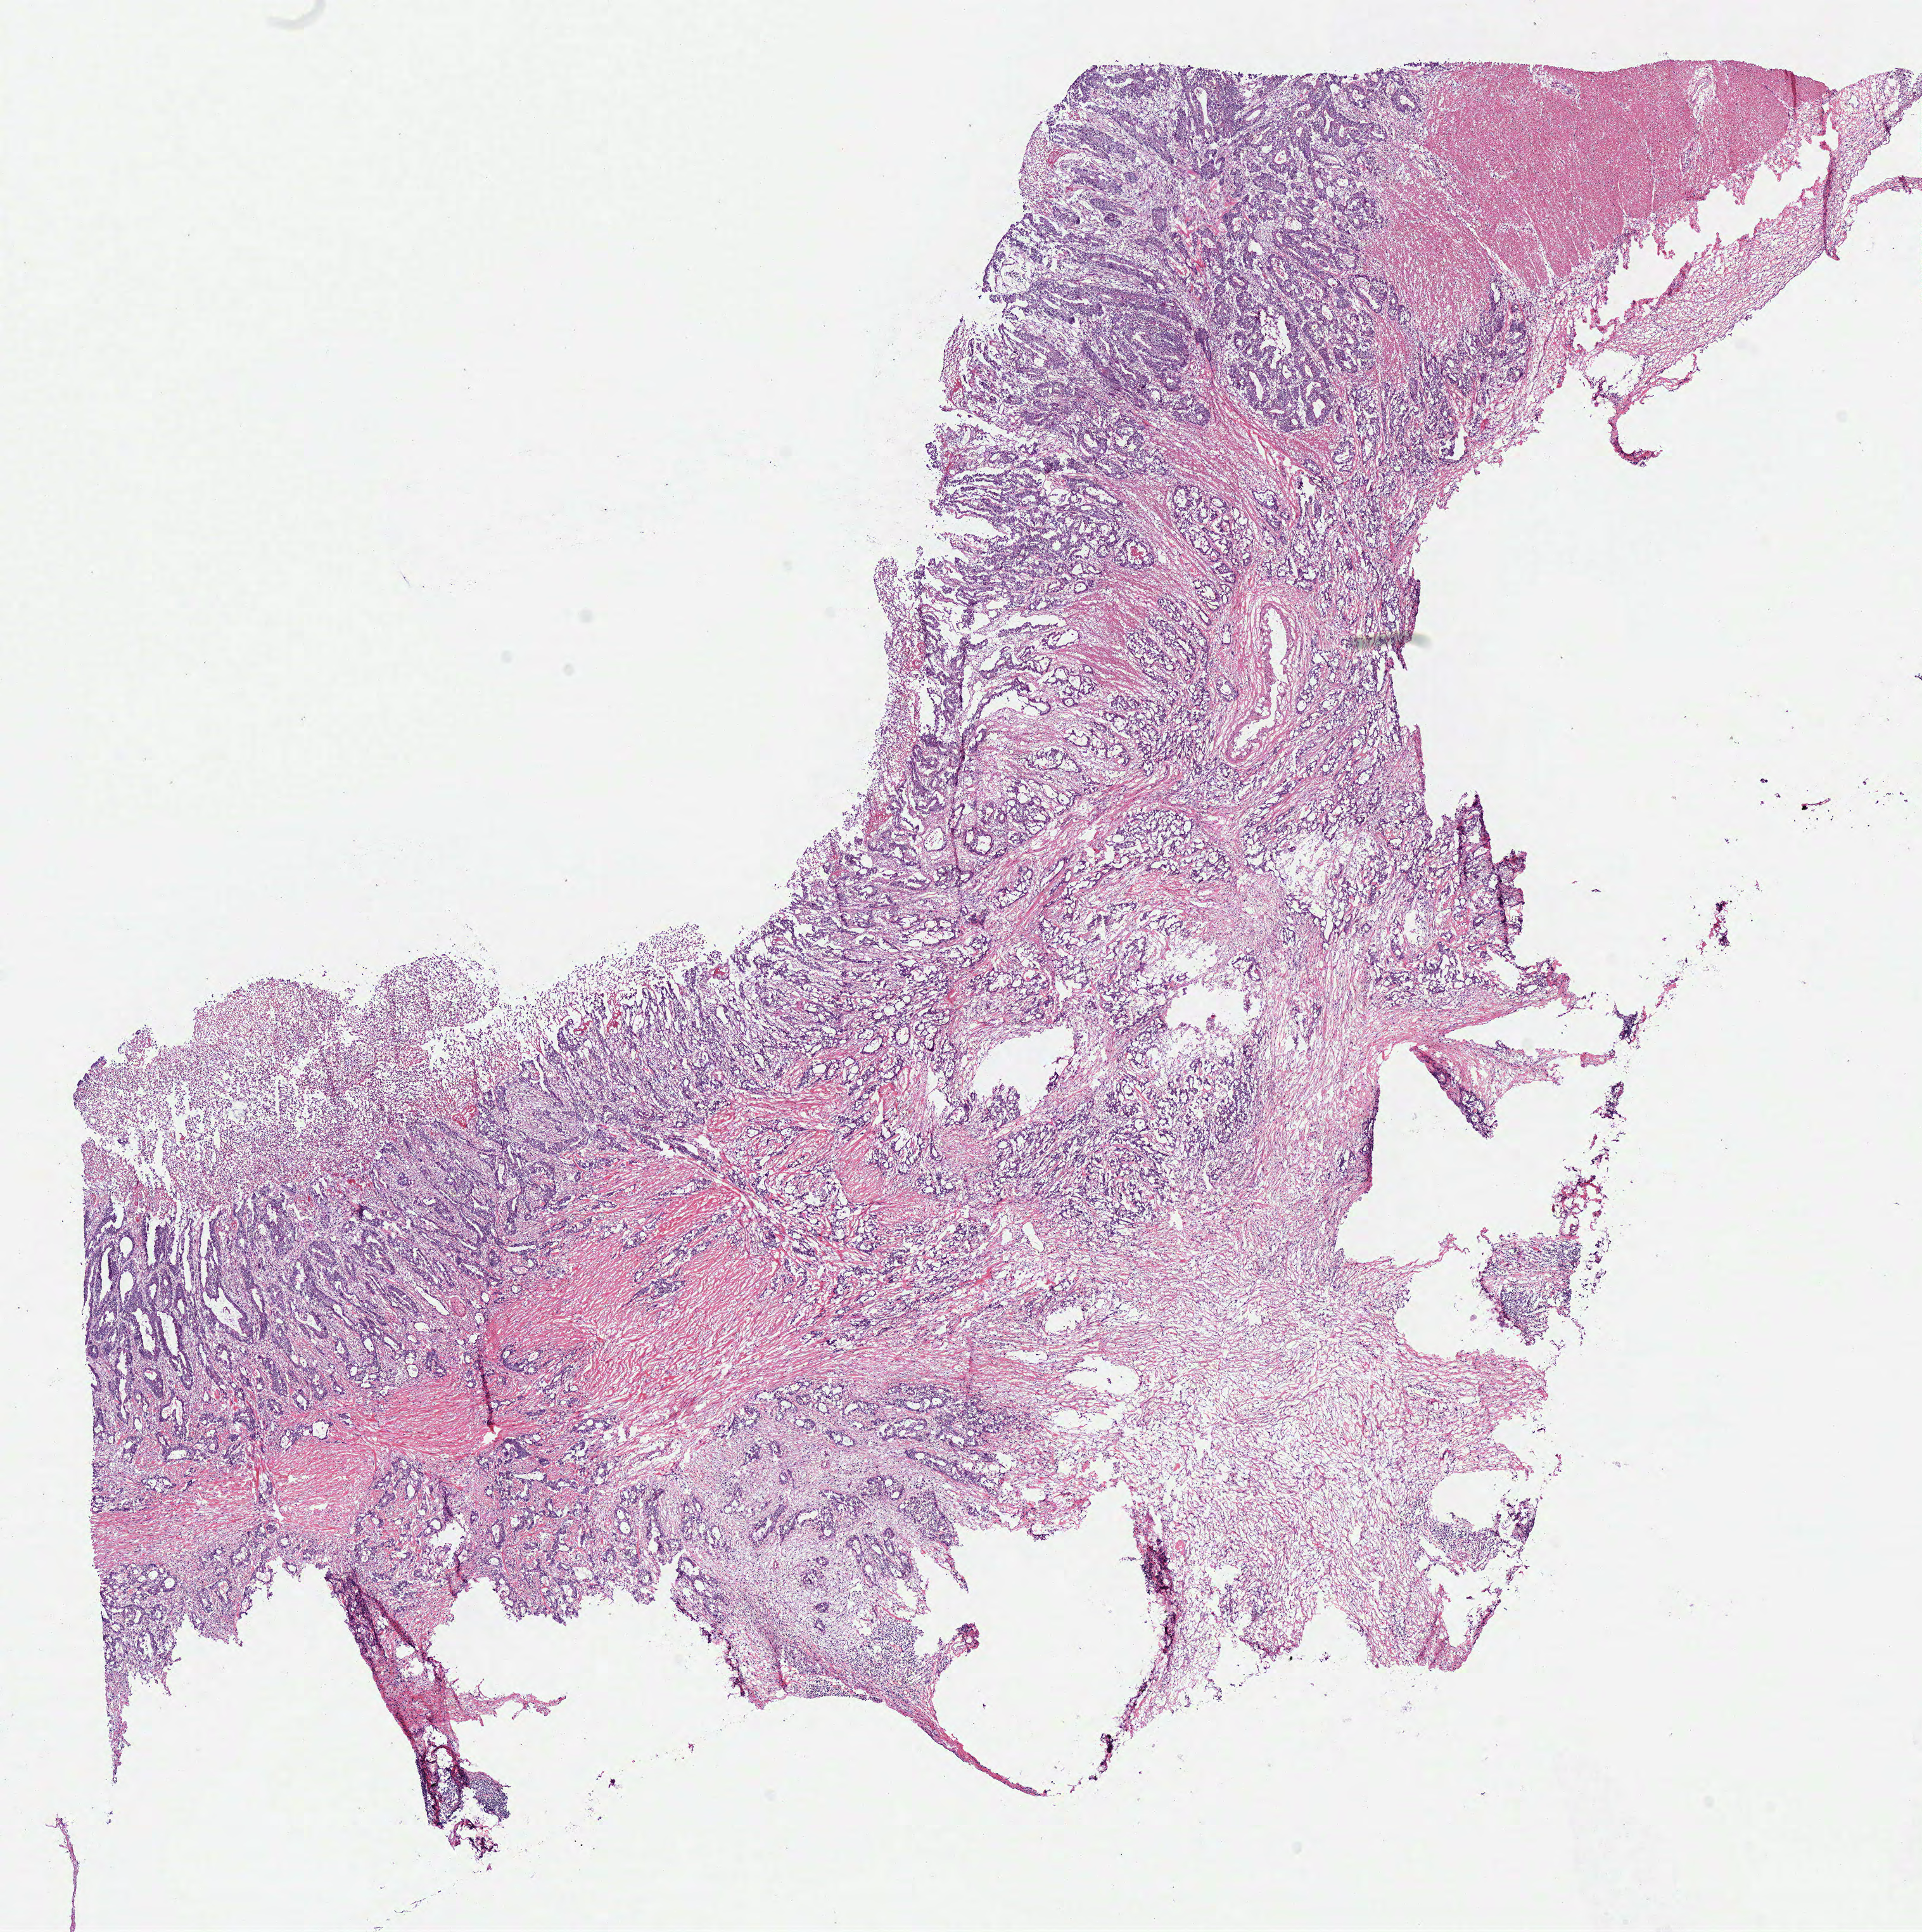
Digitized H&E-stained tissue section (whole slide), shown as a low-resolution overview of the whole scanned area (about 12.0 x 12.0 mm), frozen section, sample: primary tumour, colon. Patient: female, age at initial diagnosis 59 years. Slide review estimates, as recorded: tumour cells 82%, tumour nuclei 71%, normal cells 8%, stromal cells 8%, necrosis 2%. Inflammatory infiltration, as recorded: lymphocyte infiltration 7%, monocyte infiltration 2%, neutrophil infiltration 15%.
AJCC pathologic stage: IVA (7th edition). Lymph nodes positive (case pathology): 1 of 17 examined. Diagnosis: Adenocarcinoma, NOS (sigmoid colon).